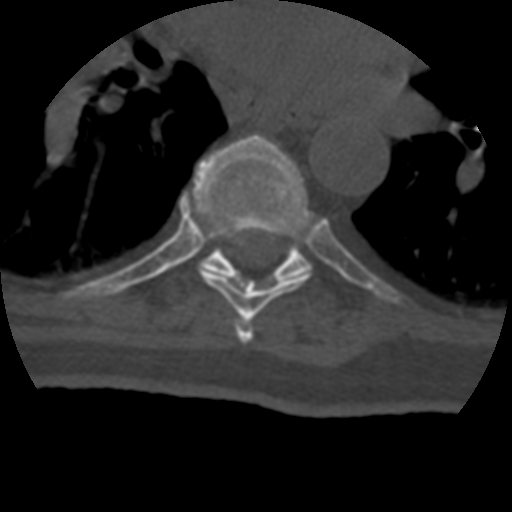
CT including the spine, one axial slice. Position 273 of 399 along the scan axis. 120 kVp. Bone window (W 1800 / L 400 HU). 512 × 512 image matrix, field of view 160 × 160 mm. Patient age 69 years. From the clinical record (not read from this slice): primary cancer: prostate.
Outlined on this slice (semi-automatically segmented with operator editing):
- T6 vertebra: bounding box [x1, y1, x2, y2] px = [235, 321, 254, 343]
- T7 vertebra: [192, 135, 317, 321]
- T8 vertebra: [201, 157, 311, 282]